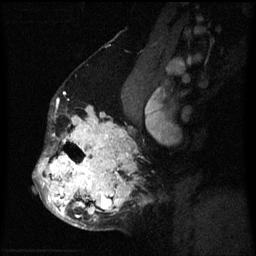
Breast MRI (dynamic contrast-enhanced), one sagittal slice. Position 38 of 60 along the scan axis. Dynamic contrast-enhanced series, image 2 of 3 at this slice position (ordered by acquisition). 1.5 T. TE 4.2 ms, TR 8 ms. 2 mm slice thickness. 256 × 256 image matrix. Female patient, age 50 years.
Outlined on this slice (semi-automatically segmented with operator editing):
- analysis volume of interest (the breast-tissue region the enhancement analysis was run in; not a lesion): bounding box [x1, y1, x2, y2] px = [33, 102, 152, 230]
- tumour enhancement mask (voxels above the 70 % enhancement threshold inside the analysis volume of interest): [37, 107, 135, 226]